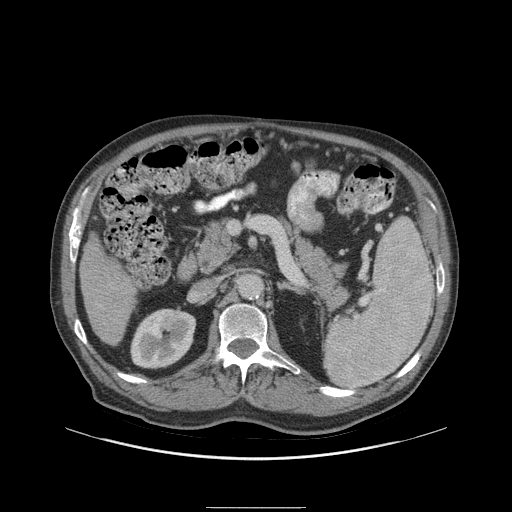
Contrast-enhanced abdominal CT (liver protocol), one axial slice; position 37 of 105 along the scan axis; reconstruction kernel STANDARD; soft-tissue window (W 400 / L 40 HU); 2.5 mm slice thickness; 512 × 512 image matrix, field of view 440 × 440 mm. Case-level facts recorded for this patient, not image findings: diagnosis: hepatocellular carcinoma (patient treated with transarterial chemoembolisation; whether this scan precedes or follows treatment is not stated here); TNM stage (as recorded): Stage-I; Child-Pugh class: A; tumour size: 5.1 cm.
Annotated regions visible in this slice (semi-automatically segmented with operator editing):
- liver parenchyma outside the tumour (the mass and vessels are separate outlines, so this box may not span the whole liver): bounding box (x1, y1, x2, y2) in pixels: (78, 234, 136, 346)